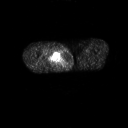
FDG PET of an extremity soft-tissue mass (from a PET/CT study), one axial slice. Slice 243 of 311 in the series (ordered by position). 3.27 mm slice thickness. 128 × 128 image matrix. Male patient, age 50 years. From the clinical record (not read from this slice): histological type: undifferentiated - pleiomorphic; grade: high; site of the primary tumour: right thigh.
Outlined on this slice (expert contour drawn on MRI and transferred to this co-registered scan by the dataset authors):
- gross tumour volume including surrounding oedema: box from (x=41, y=49) to (x=59, y=63) px
- gross tumour volume (mass): (x=47, y=51)–(x=59, y=62)